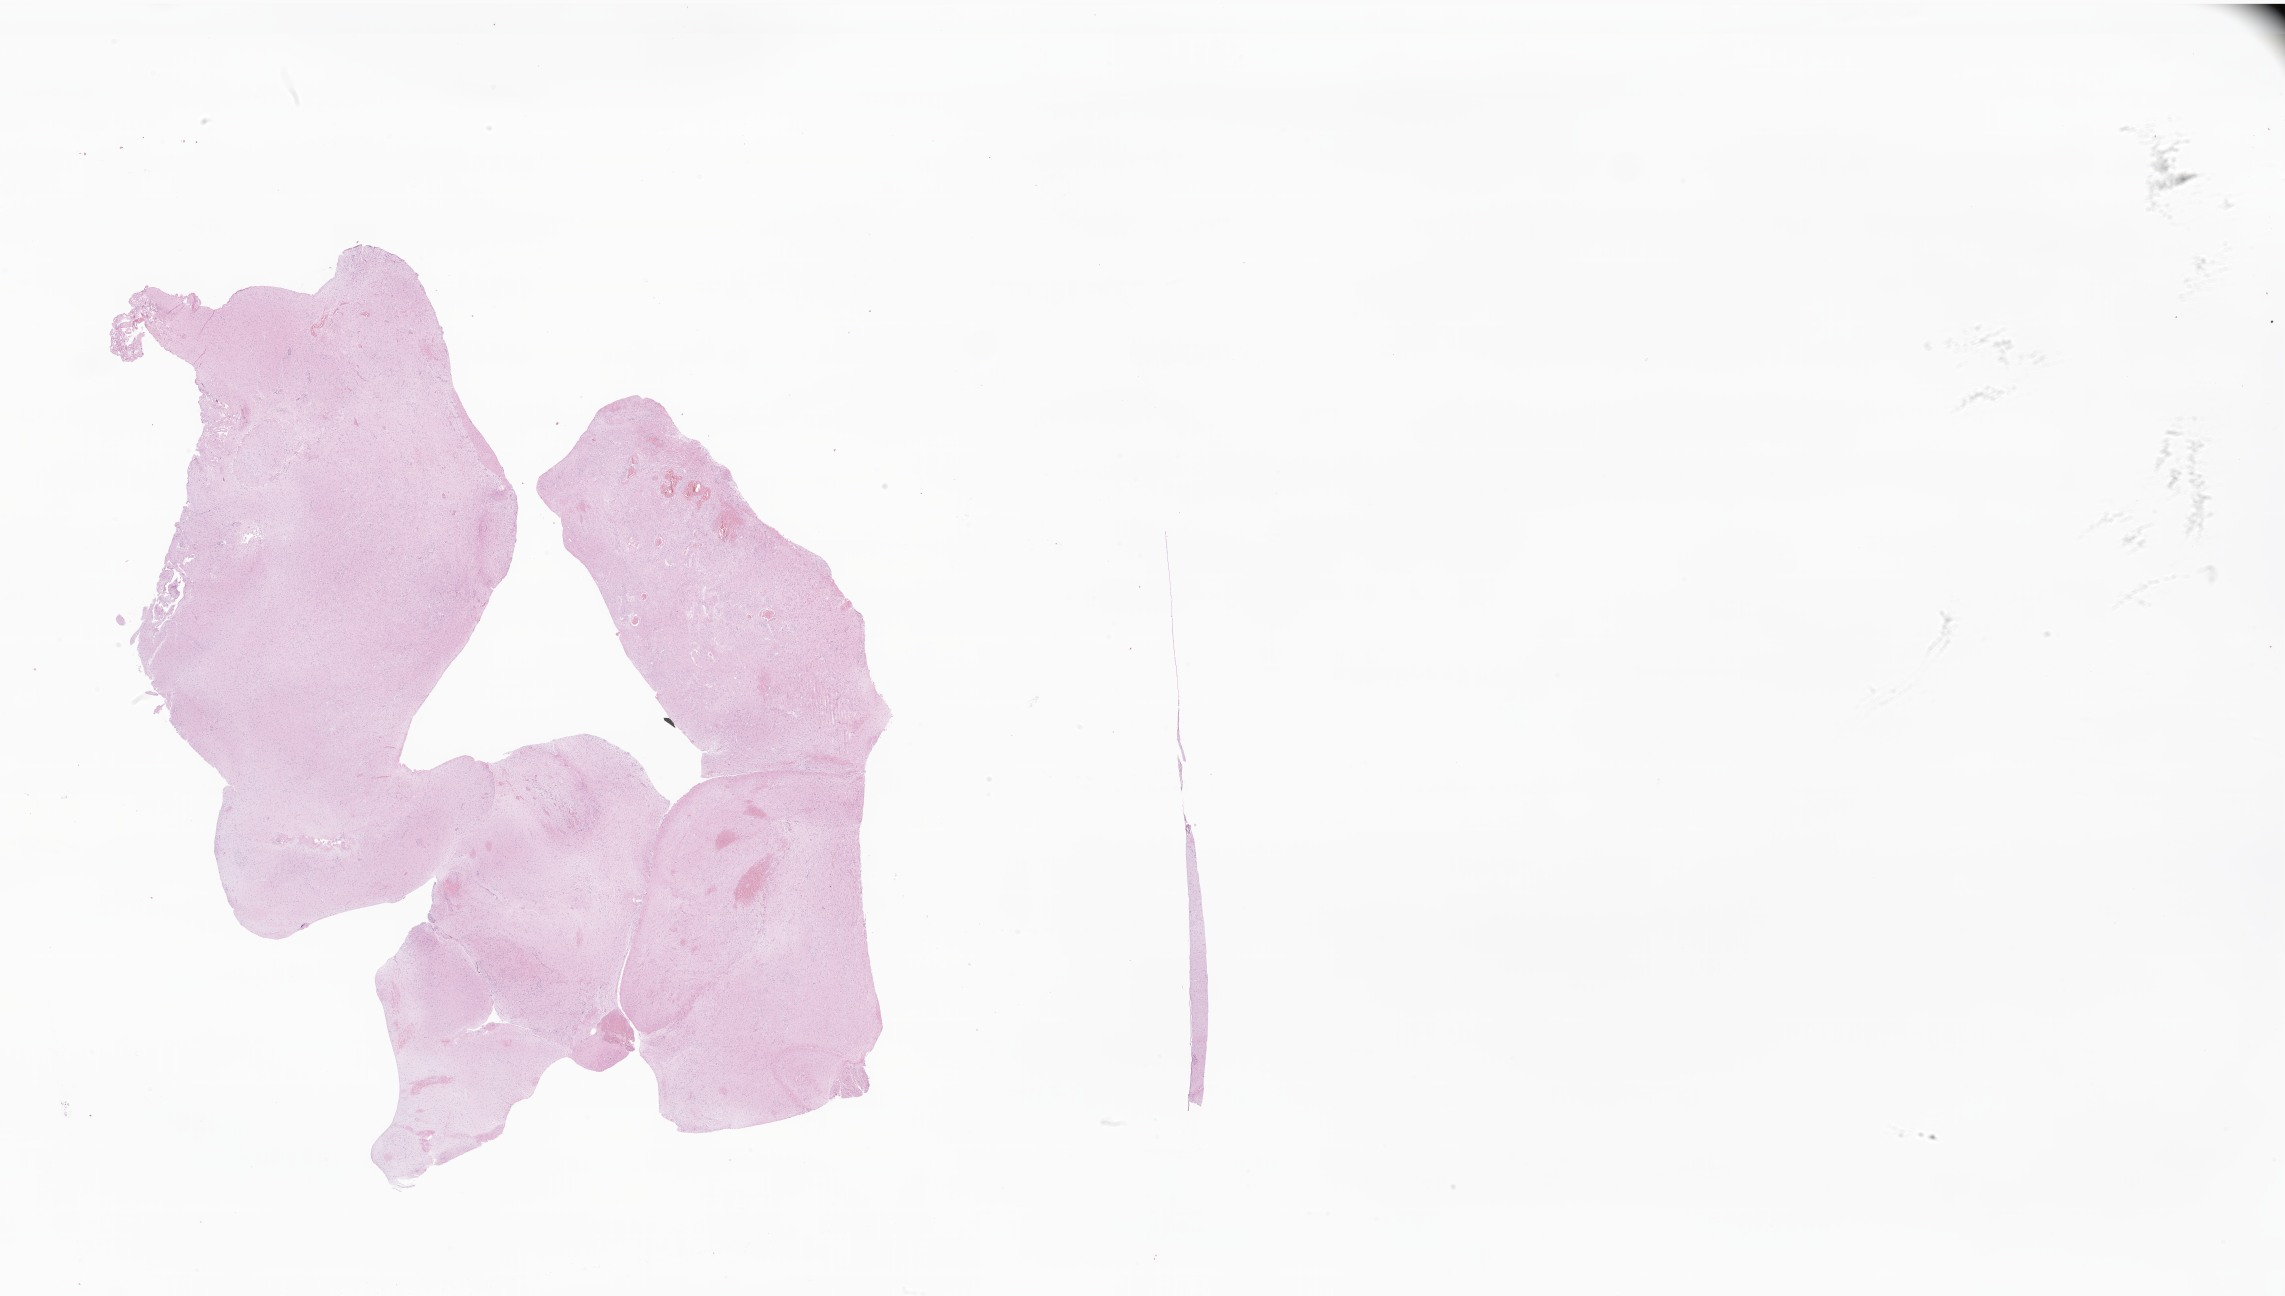
Haematoxylin and eosin whole-slide image of tumor tissue from the brain — low-resolution overview of the scanned area, about 38.5 x 21.9 mm, formalin-fixed paraffin-embedded section. Patient: female, age 225 months (18 years 9 months).
Diagnosis (ICD-O-3 morphology term): Neoplasm, malignant.